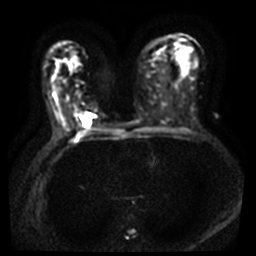
Breast MRI, one axial slice. Slice 26 of 40 in the series (ordered by position). Diffusion-weighted series; image 2 of 4 stored at this slice position (different b-values; order by instance number). 3 T. 5 mm slice thickness. 256 × 256 image matrix, field of view 340 × 340 mm. Female patient.
Outlined on this slice (manually delineated by an expert):
- tumour on diffusion-weighted imaging: bounding box [x1, y1, x2, y2] px = [82, 113, 92, 125]